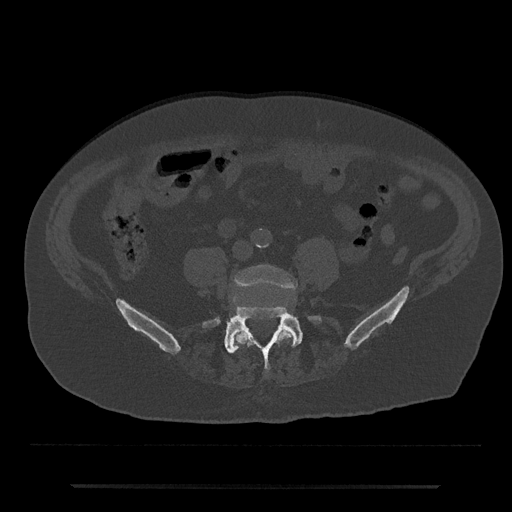
CT including the spine, one axial slice; reconstruction kernel Br40s/3; 120 kVp; bone window (W 1800 / L 400 HU); 0.5 mm slice thickness; 512 × 512 image matrix, field of view 434 × 434 mm. Patient: male, 80 years. From the clinical record (not read from this slice): primary cancer: prostate.
Annotated regions visible in this slice (semi-automatically segmented with operator editing):
- L4 vertebra: bounding box <233,265,296,346> (left, top, right, bottom; pixels)
- L5 vertebra: <202,306,322,370>